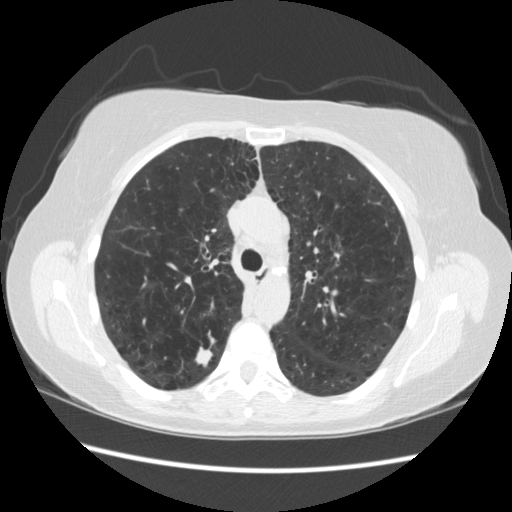
Low-dose screening chest CT, axial slice; third screening round (two years after baseline); lung window (W 1500 / L -600 HU); 2.5 mm slice thickness; 120 kVp; slice 74 of 235 in the series. Female participant, aged 55 years at enrolment. Current smoker at enrolment.
• Expert reader's lesion annotation, bounding box <181,332,228,374> (left, top, right, bottom; pixels).
• Reader record for this screening exam (exam-level; its link to the box is not recorded): non-calcified nodule or mass ≥4 mm, right upper lobe, 11 × 11 mm, poorly defined margins, soft tissue attenuation, pre-existing on the prior screen: no.
• Lung cancer was diagnosed 96 days after this screen: small cell carcinoma, NOS, right upper lobe.